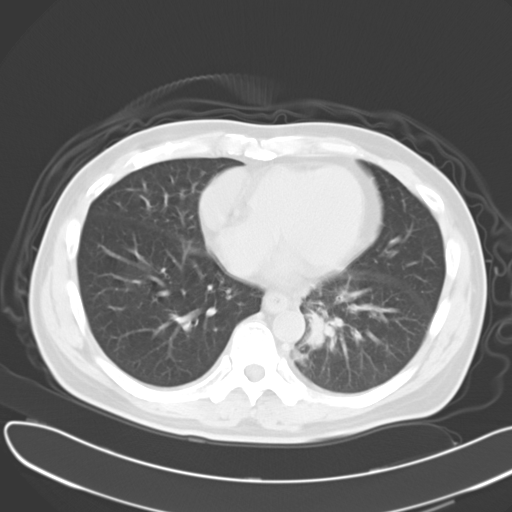
Chest CT, one axial slice. Slice 12 of 30 in the series (ordered by position). Lung window (W 1500 / L -600 HU). 10 mm slice thickness. 512 × 512 image matrix, field of view 376 × 376 mm. Male patient, age 55 years. Case-level facts recorded for this patient, not image findings: clinical TNM (as recorded): T2 N3 M0.
Outlined on this slice (rectangle marked by the reading radiologist):
- lung tumour (recorded histology: small cell carcinoma): bounding box <305,306,346,357> (left, top, right, bottom; pixels)